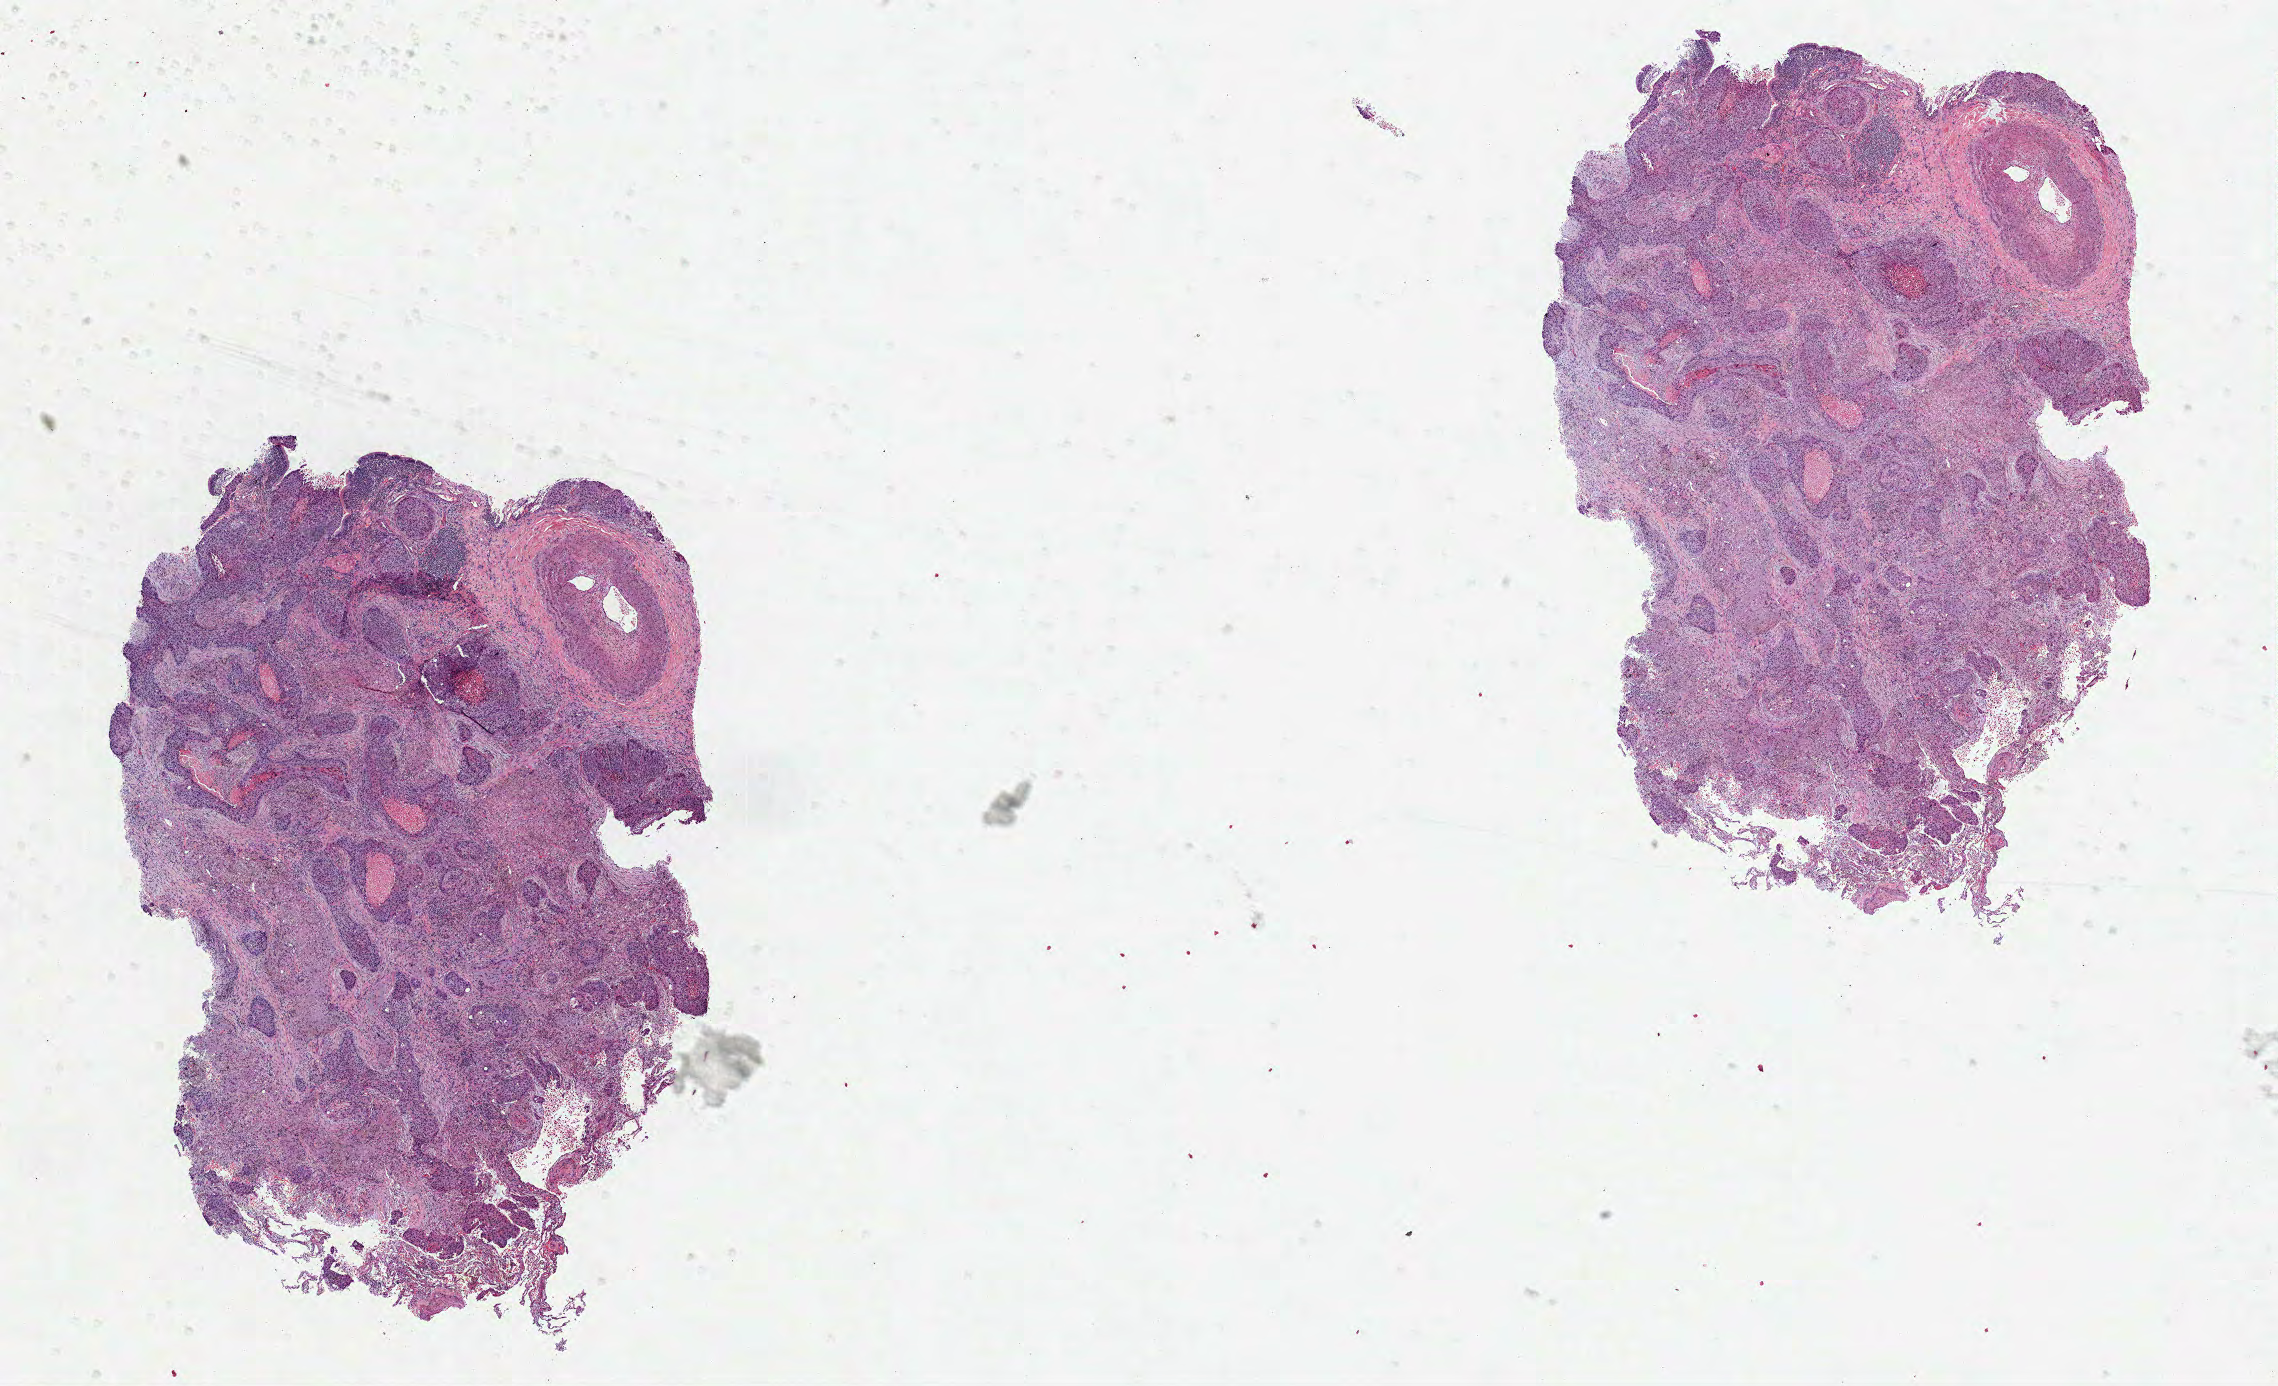
Whole-slide histology image, Hematoxylin and eosin (H&E) stained, low-resolution overview of the scanned area, about 18.4 x 11.2 mm; FFPE section; lung, primary tumour sample. Female patient; age at initial diagnosis 68 years.
AJCC pathologic stage: IA (7th edition). TNM: T1 N0 MX. Pathologic diagnosis: Squamous cell carcinoma, NOS (upper lobe, lung).